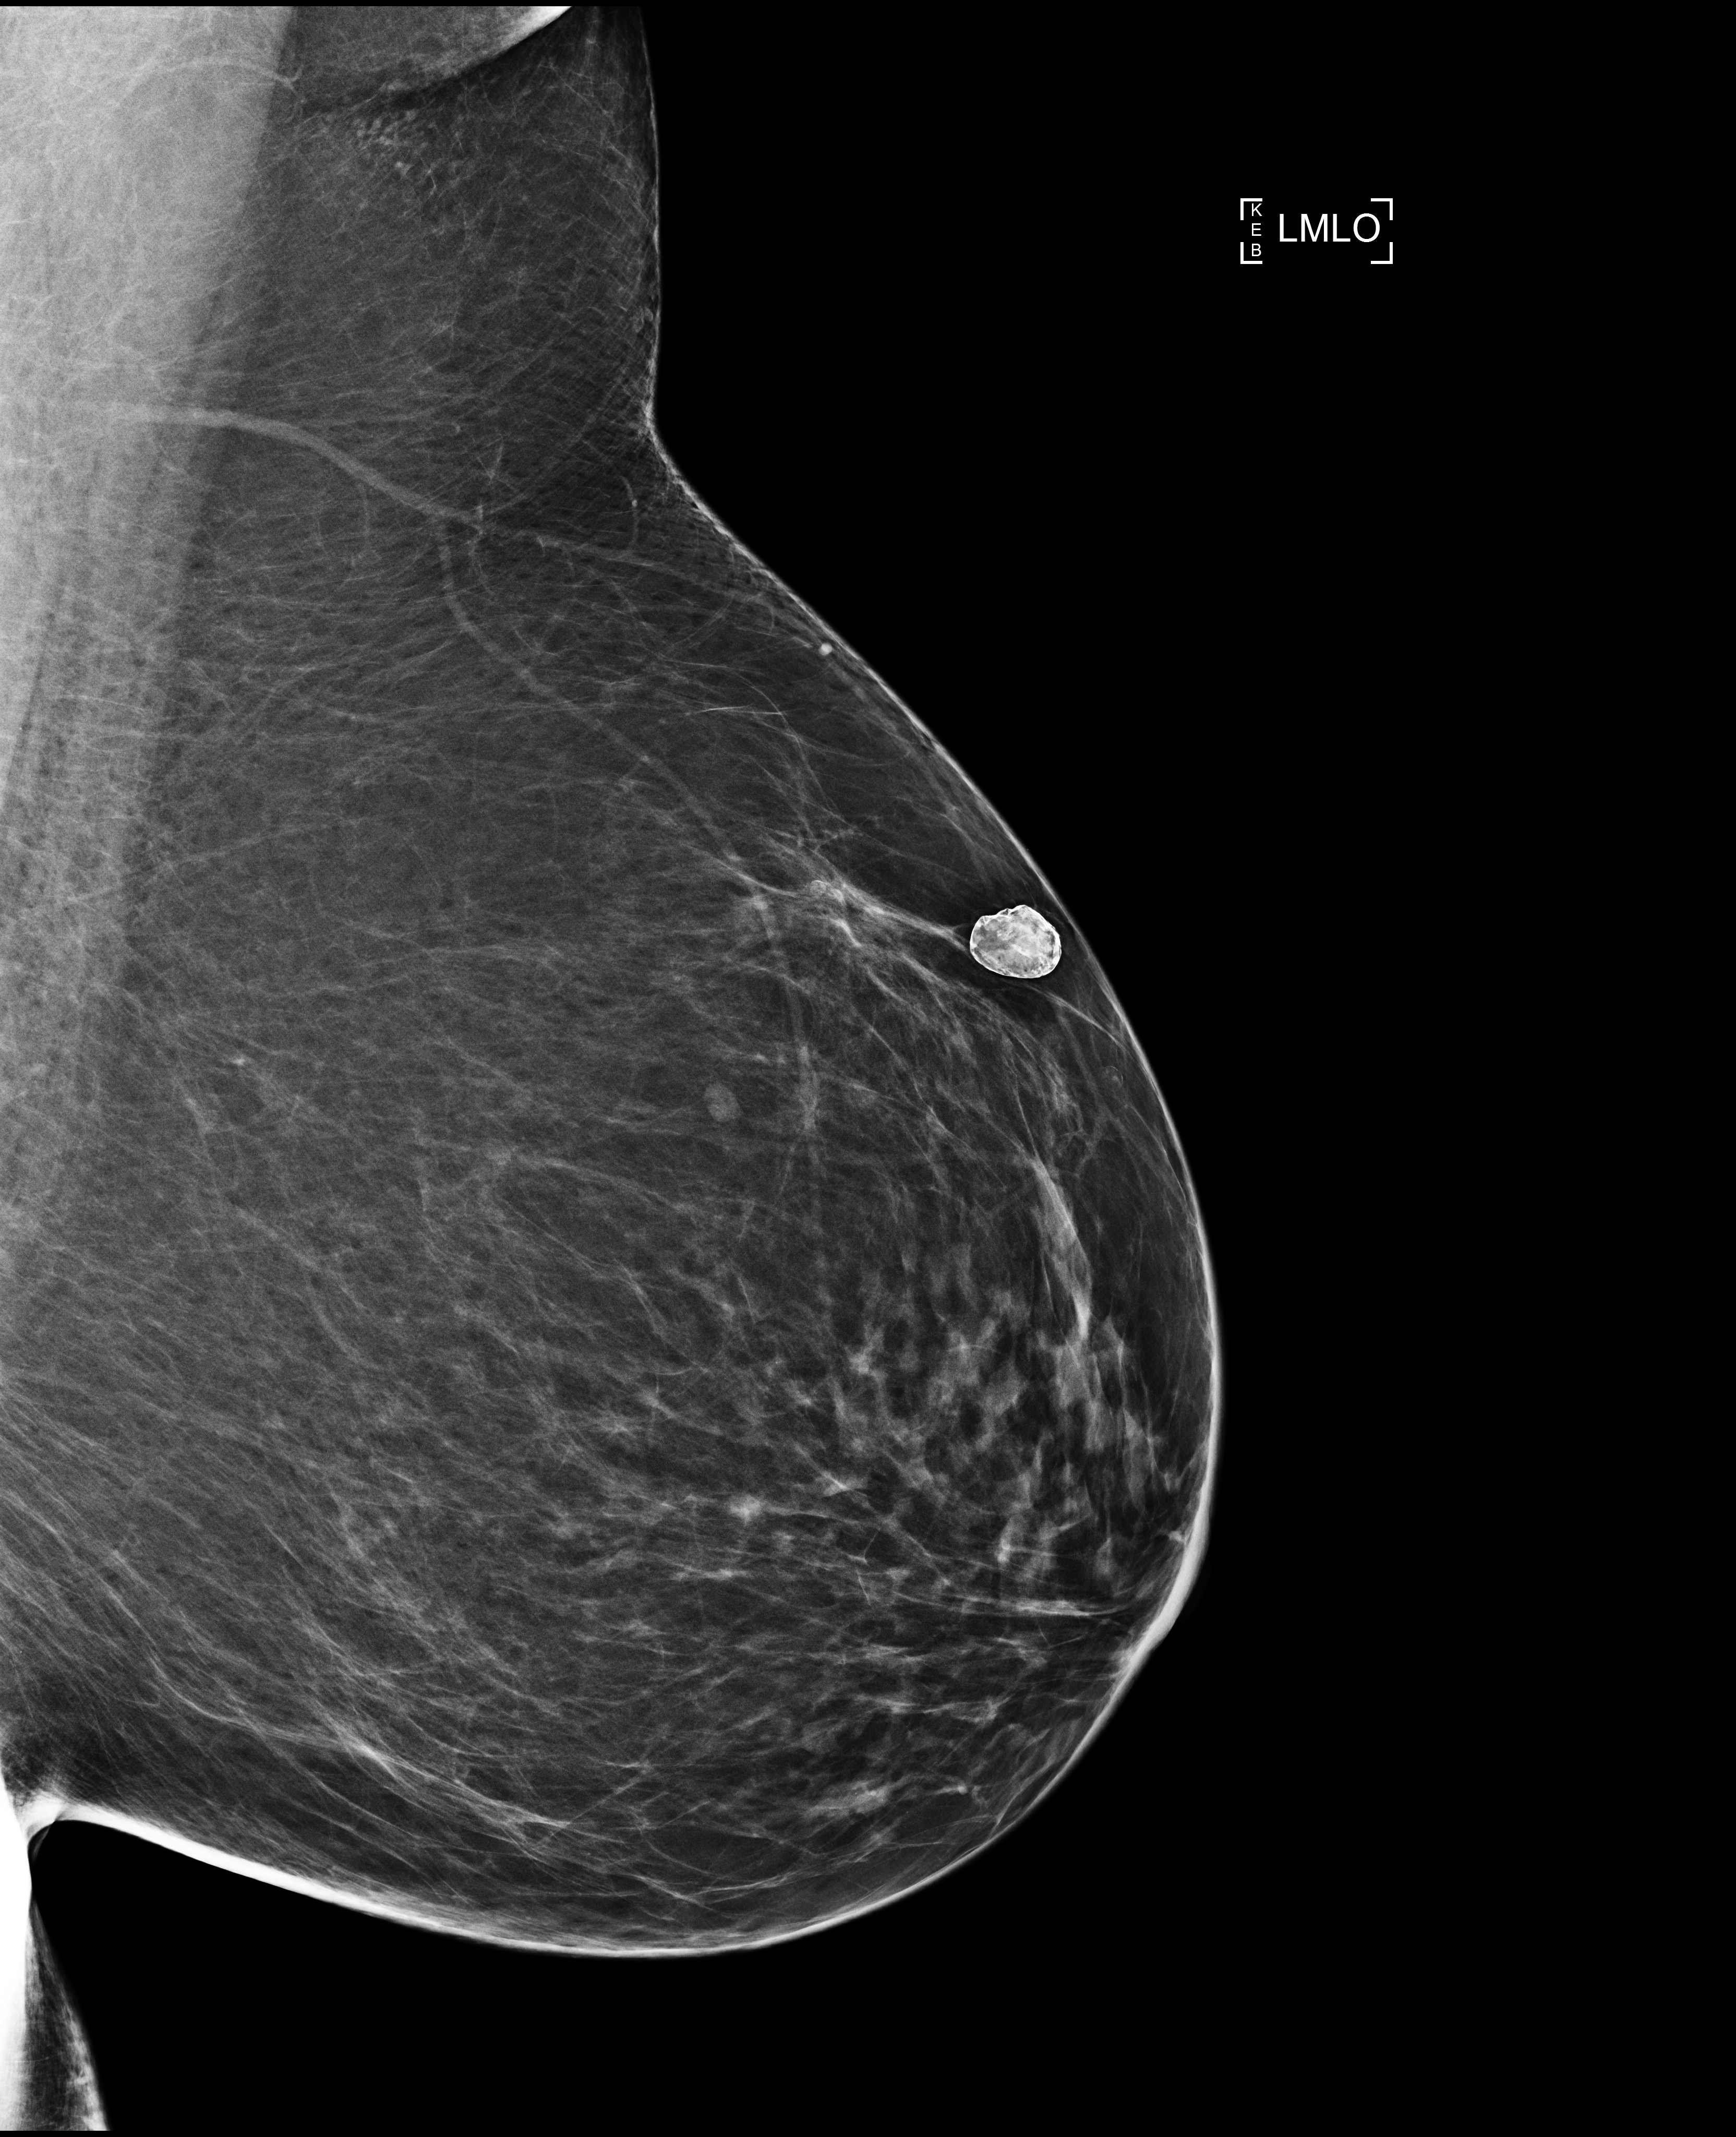
Screening examination; compressed breast thickness 74 mm. Female patient, age 67 years.
Image type: full-field digital mammogram. Breast: left. Projection: mediolateral oblique (MLO) view.